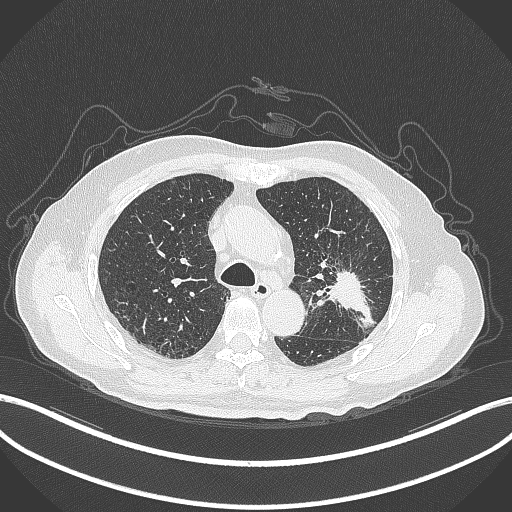
Chest CT, one axial slice. Lung window (W 1500 / L -600 HU). 1 mm slice thickness. 512 × 512 image matrix, field of view 400 × 400 mm. Male patient, age 79 years. Case-level facts recorded for this patient, not image findings: clinical TNM (as recorded): T2a N1 M1; histopathological grade: G3.
Structures marked on this image (bounding box drawn by a radiologist):
- lung tumour (recorded histology: adenocarcinoma): bounding box (x1, y1, x2, y2) in pixels: (315, 268, 376, 331)